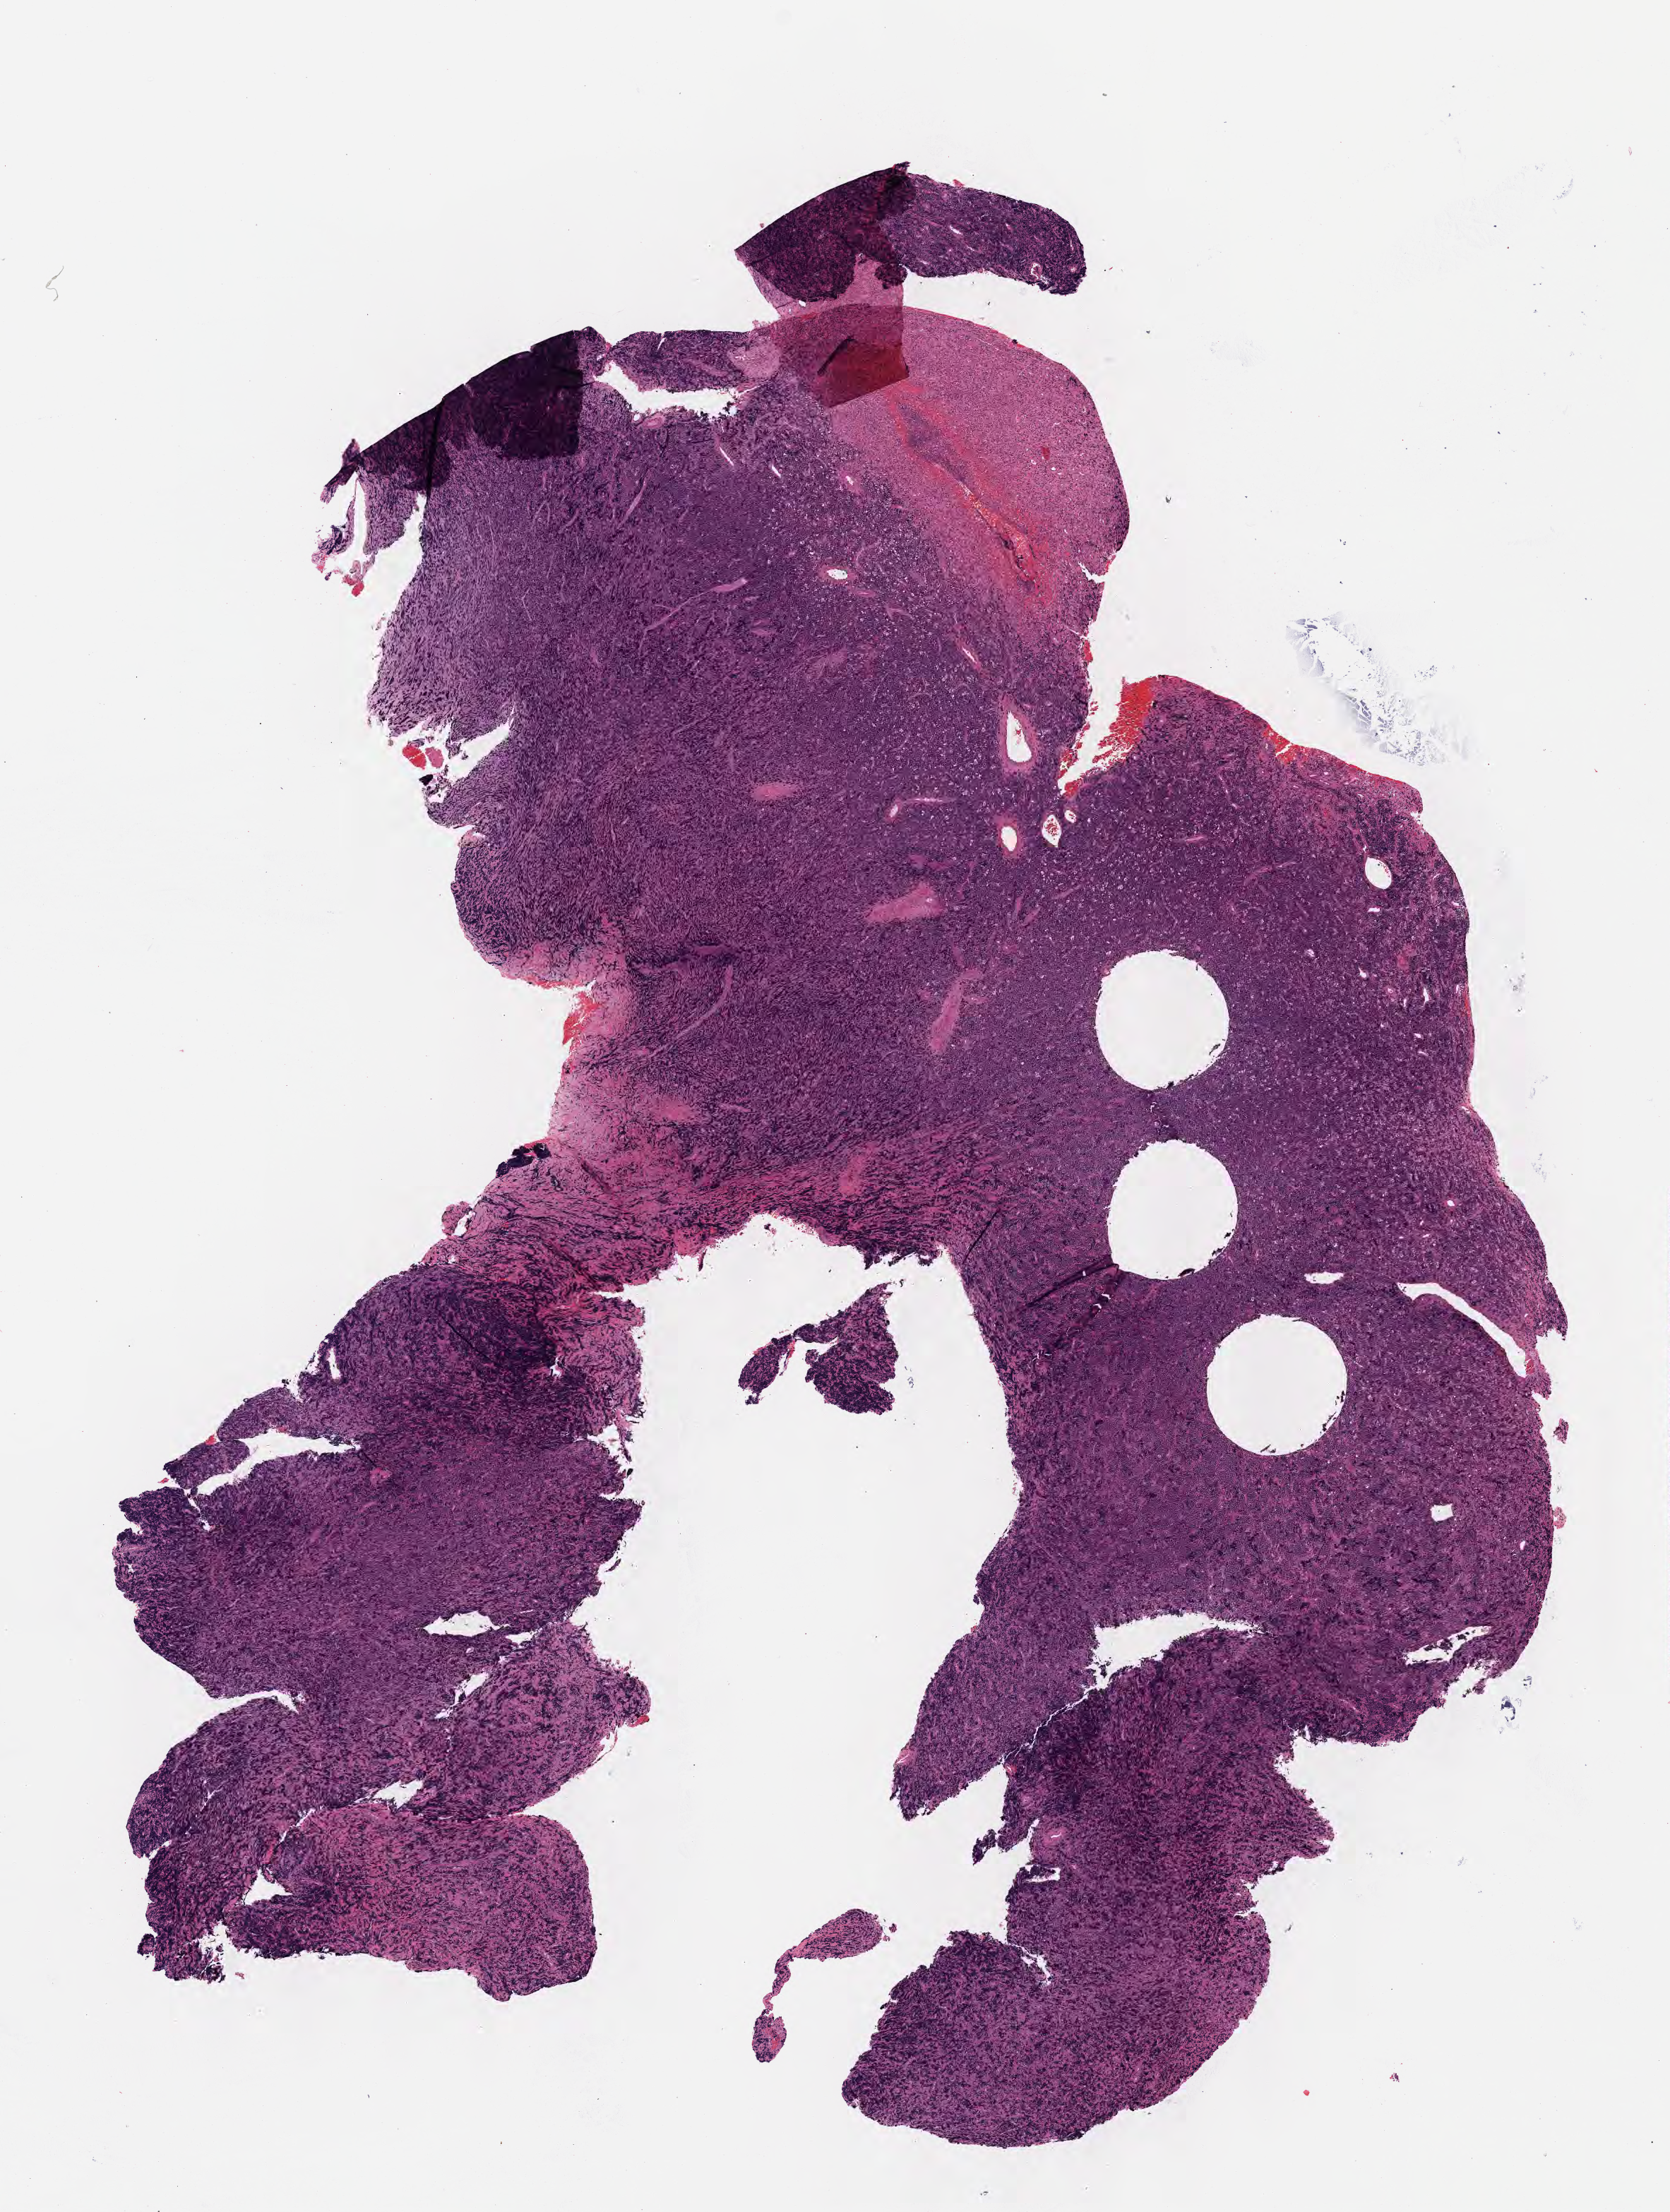
Hematoxylin and eosin (H&E) whole-slide image — shown as a low-resolution overview of the whole scanned area (about 9.6 x 12.7 mm); FFPE section; primary tumor; anatomic site: mouth. Female patient; age at initial diagnosis 7 years.
Histologic diagnosis: Diffuse large B-cell lymphoma, NOS.